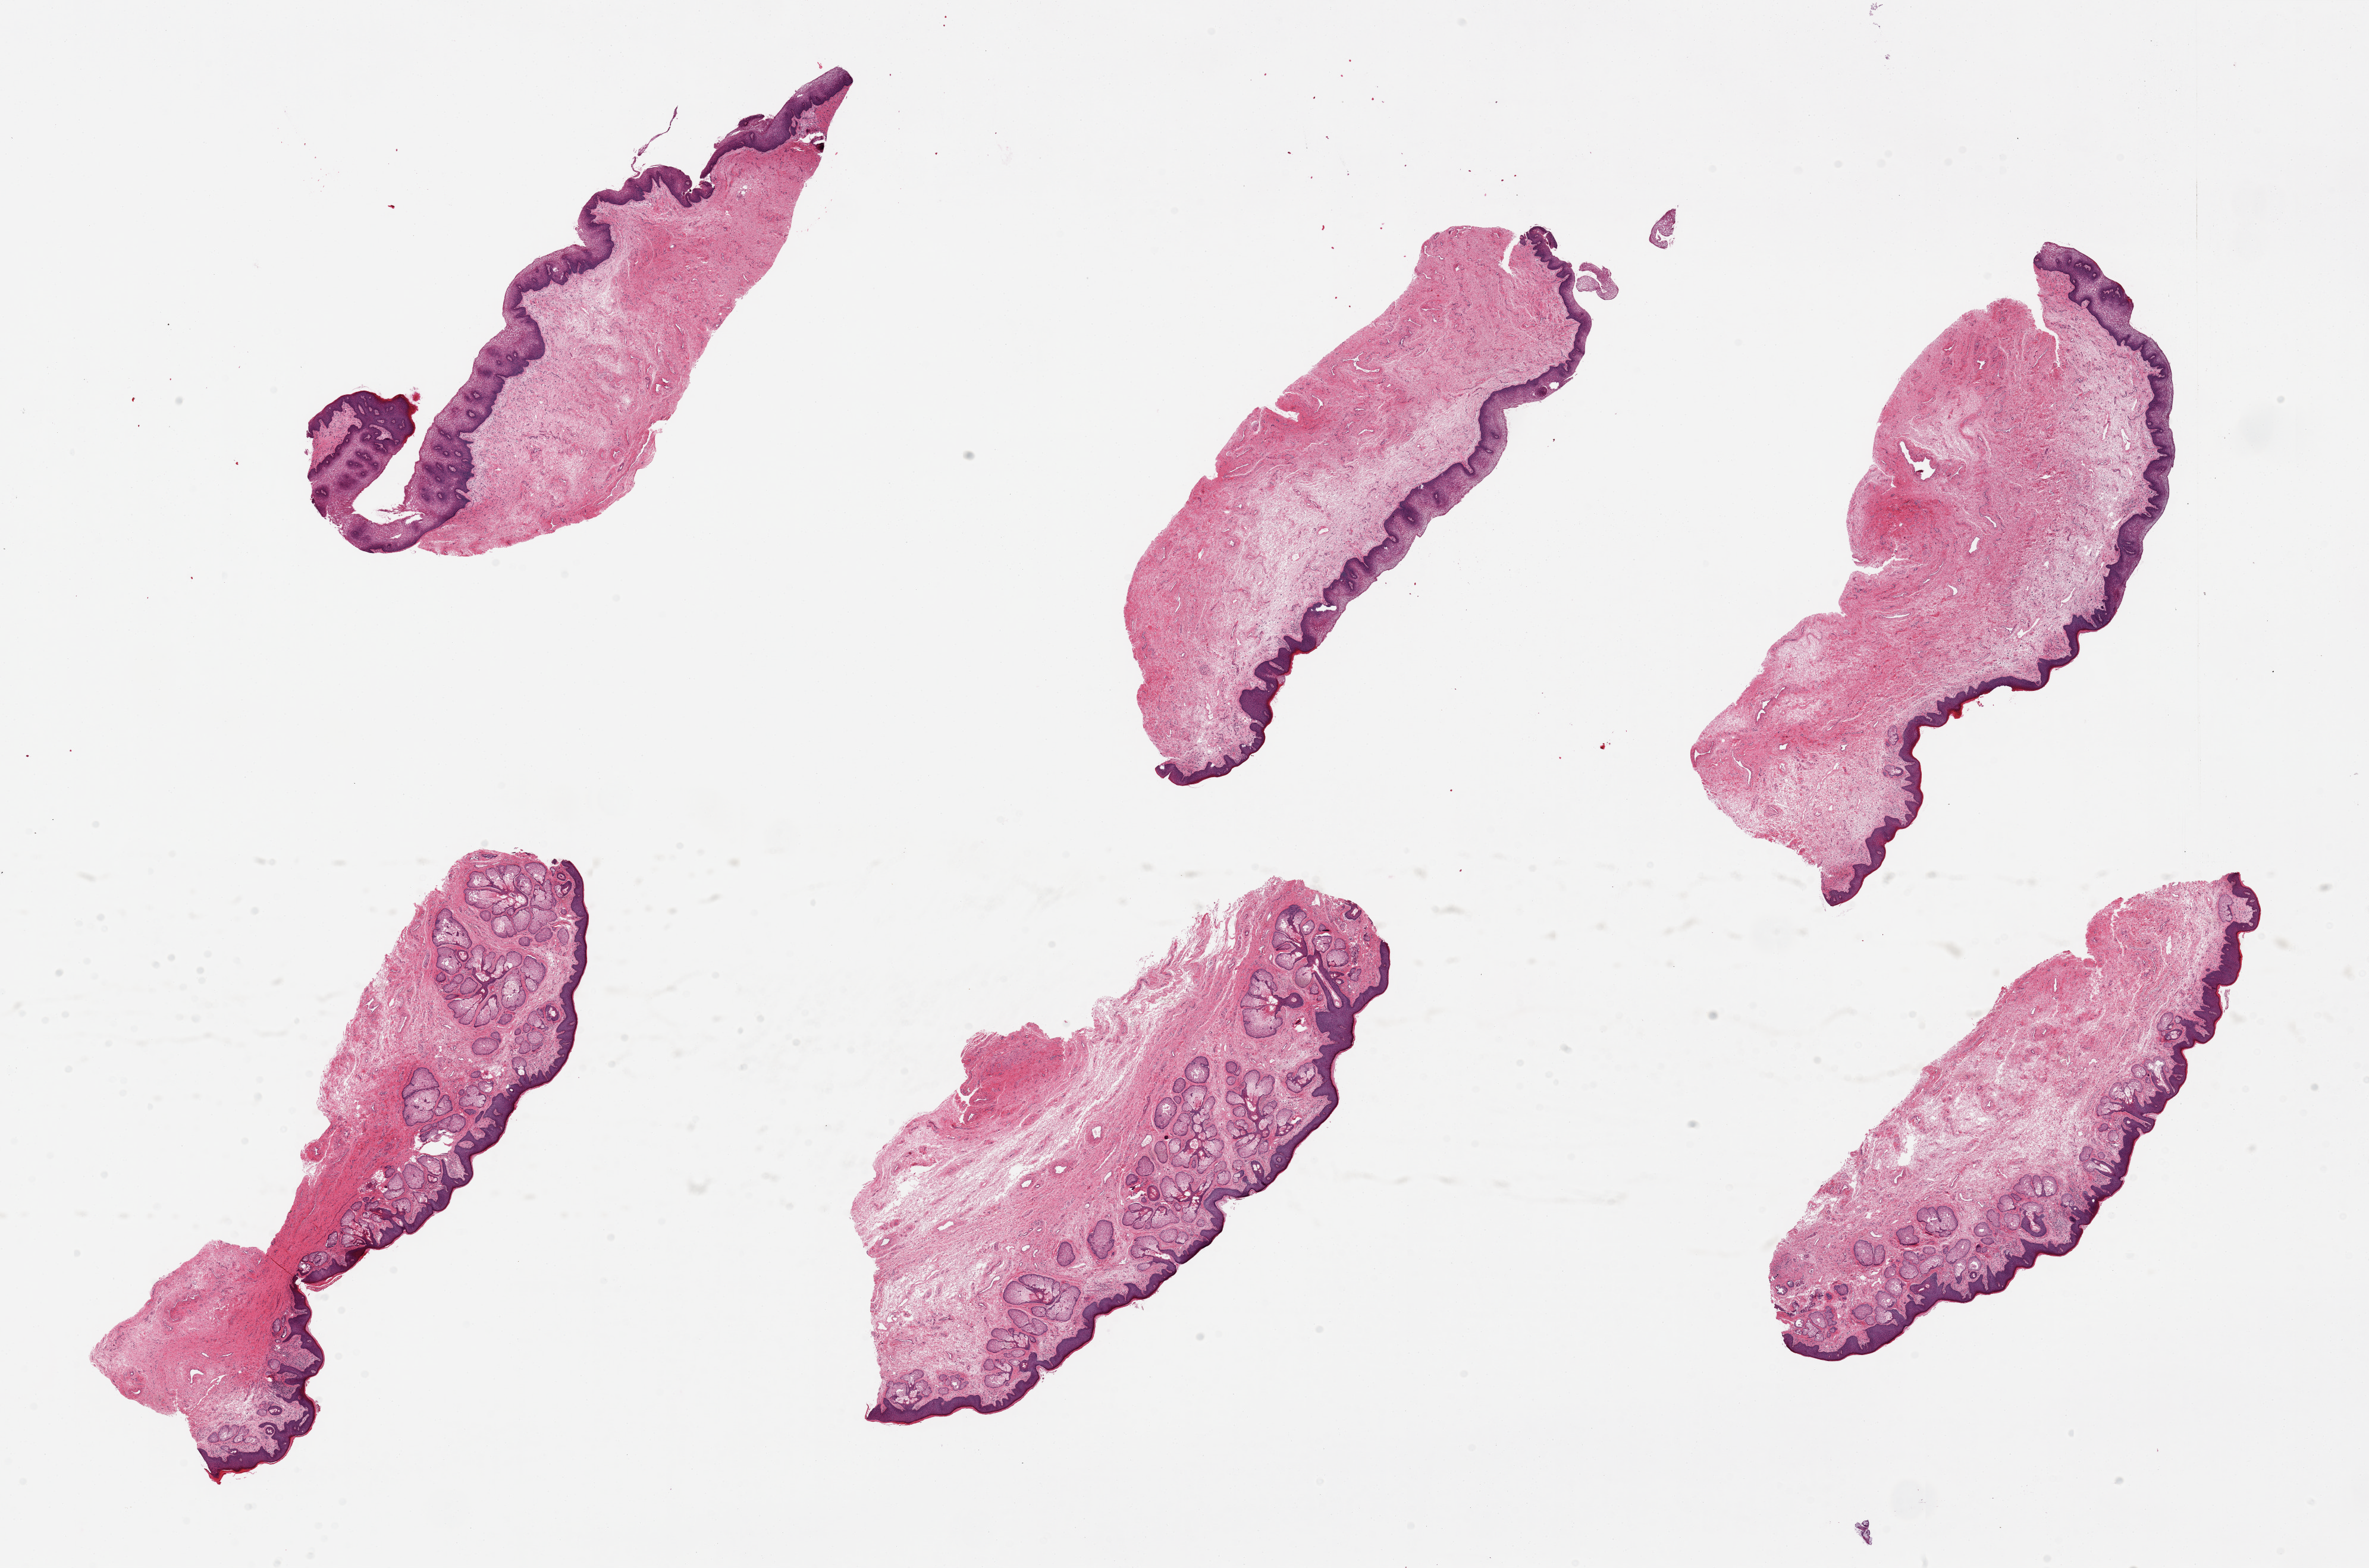
Hematoxylin and eosin (H&E) whole-slide image, brightfield, shown as a low-resolution overview of the whole scanned area (about 31.5 x 20.9 mm, from a 20x scan). PAXgene-fixed, paraffin-embedded tissue. Target tissue: vagina. Donor tissue sample. Female donor.
Reviewer comment on this tissue sample: 6 pieces. up to 9x4mm; 3 are vagina; 3 have abundant sebaceous glands, therefore vulva was sampled.